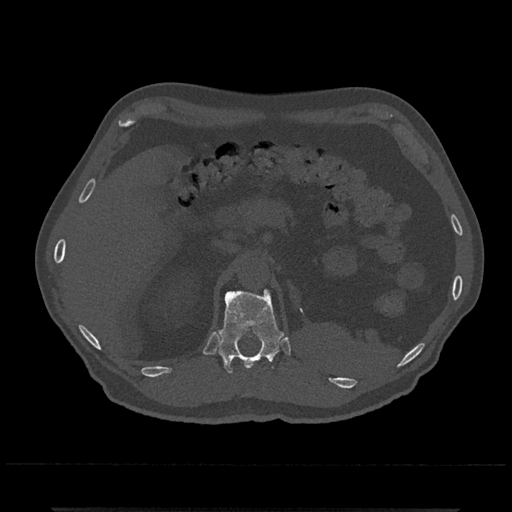
CT including the spine, one axial slice. Position 438 of 797 along the scan axis. Reconstruction kernel Br40s/3. 120 kVp. Bone window (W 1800 / L 400 HU). 0.5 mm slice thickness. 512 × 512 image matrix. Male patient, age 67 years. Case-level facts recorded for this patient, not image findings: primary cancer: prostate.
Outlined on this slice (semi-automatically segmented with operator editing):
- T12 vertebra: bounding box <218,289,284,373> (left, top, right, bottom; pixels)